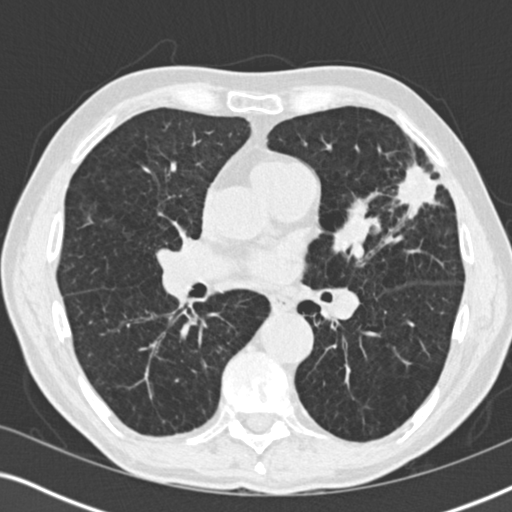
Low-dose screening chest CT, one axial slice; position 100 of 196 along the scan axis; lung window (W 1500 / L -600 HU); 2 mm slice thickness; 512 × 512 image matrix, field of view 330 × 330 mm.
Annotated regions visible in this slice (outlined manually by an expert reader):
- lesion 1 (tumor, upper lobe of left lung): box from (x=397, y=165) to (x=439, y=206) px